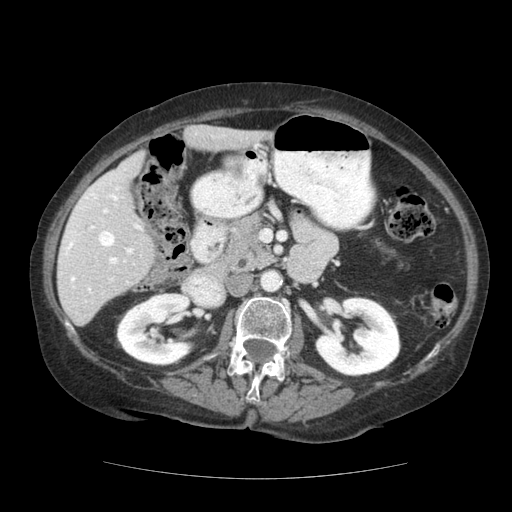
Contrast-enhanced abdominal CT (liver protocol), one axial slice; position 59 of 111 along the scan axis; reconstruction kernel STANDARD; 140 kVp; soft-tissue window (W 400 / L 40 HU); 512 × 512 image matrix, field of view 360 × 360 mm. Case-level facts recorded for this patient, not image findings: diagnosis: hepatocellular carcinoma (patient treated with transarterial chemoembolisation; whether this scan precedes or follows treatment is not stated here); TNM stage (as recorded): Stage-I; Child-Pugh class: A; tumour nodularity: uninodular; tumour size: 7.3 cm.
Annotated regions visible in this slice (semi-automatically segmented with operator editing):
- liver parenchyma outside the tumour (the mass and vessels are separate outlines, so this box may not span the whole liver): bounding box (x1, y1, x2, y2) in pixels: (58, 125, 272, 326)
- liver vessels: (64, 169, 142, 293)